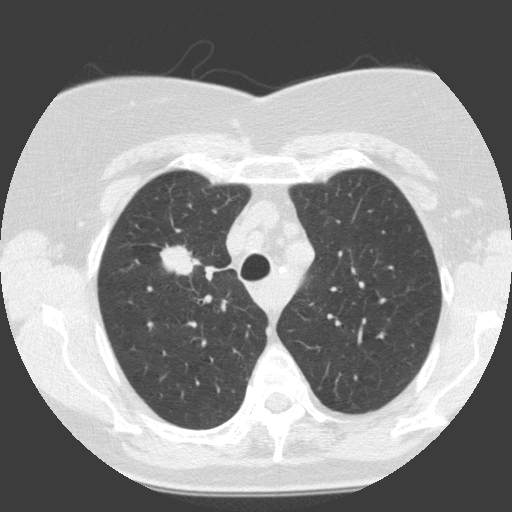
Low-dose screening chest CT, axial slice, baseline screening round, lung window (W 1500 / L -600 HU), standard (soft-tissue) reconstruction kernel (C), slice 37 of 146 in the series, 512 × 512 image matrix. Female participant, aged 68 years at enrolment. Current smoker at enrolment.
Expert-annotated lung lesion, box from (x=155, y=236) to (x=205, y=282) px. The exam's reader record, not a measurement of the box and not confirmed to be the same lesion: non-calcified nodule or mass ≥4 mm, right upper lobe, 19 × 12 mm, smooth margins, soft tissue attenuation. Participant outcome: lung cancer diagnosed 30 days after this screen — squamous cell carcinoma, NOS, right upper lobe, moderately differentiated (G2), stage IA (AJCC 6th edition), 28 mm at pathology.